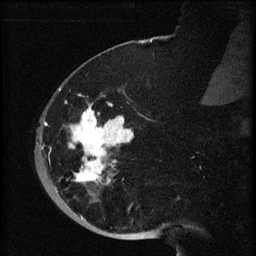
Breast MRI (dynamic contrast-enhanced), one sagittal slice; slice 20 of 60 in the series (ordered by position); dynamic contrast-enhanced series, image 2 of 3 at this slice position (ordered by acquisition); 1.5 T; TE 4.2 ms, TR 8.2 ms; 2 mm slice thickness; 256 × 256 image matrix, field of view 180 × 180 mm. Patient: female, 71 years.
Structures marked on this image (semi-automatic segmentation, software-assisted and operator-edited):
- analysis volume of interest (the breast-tissue region the enhancement analysis was run in; not a lesion): bounding box (x1, y1, x2, y2) in pixels: (40, 72, 148, 196)
- tumour enhancement mask (voxels above the 70 % enhancement threshold inside the analysis volume of interest): (42, 88, 134, 185)